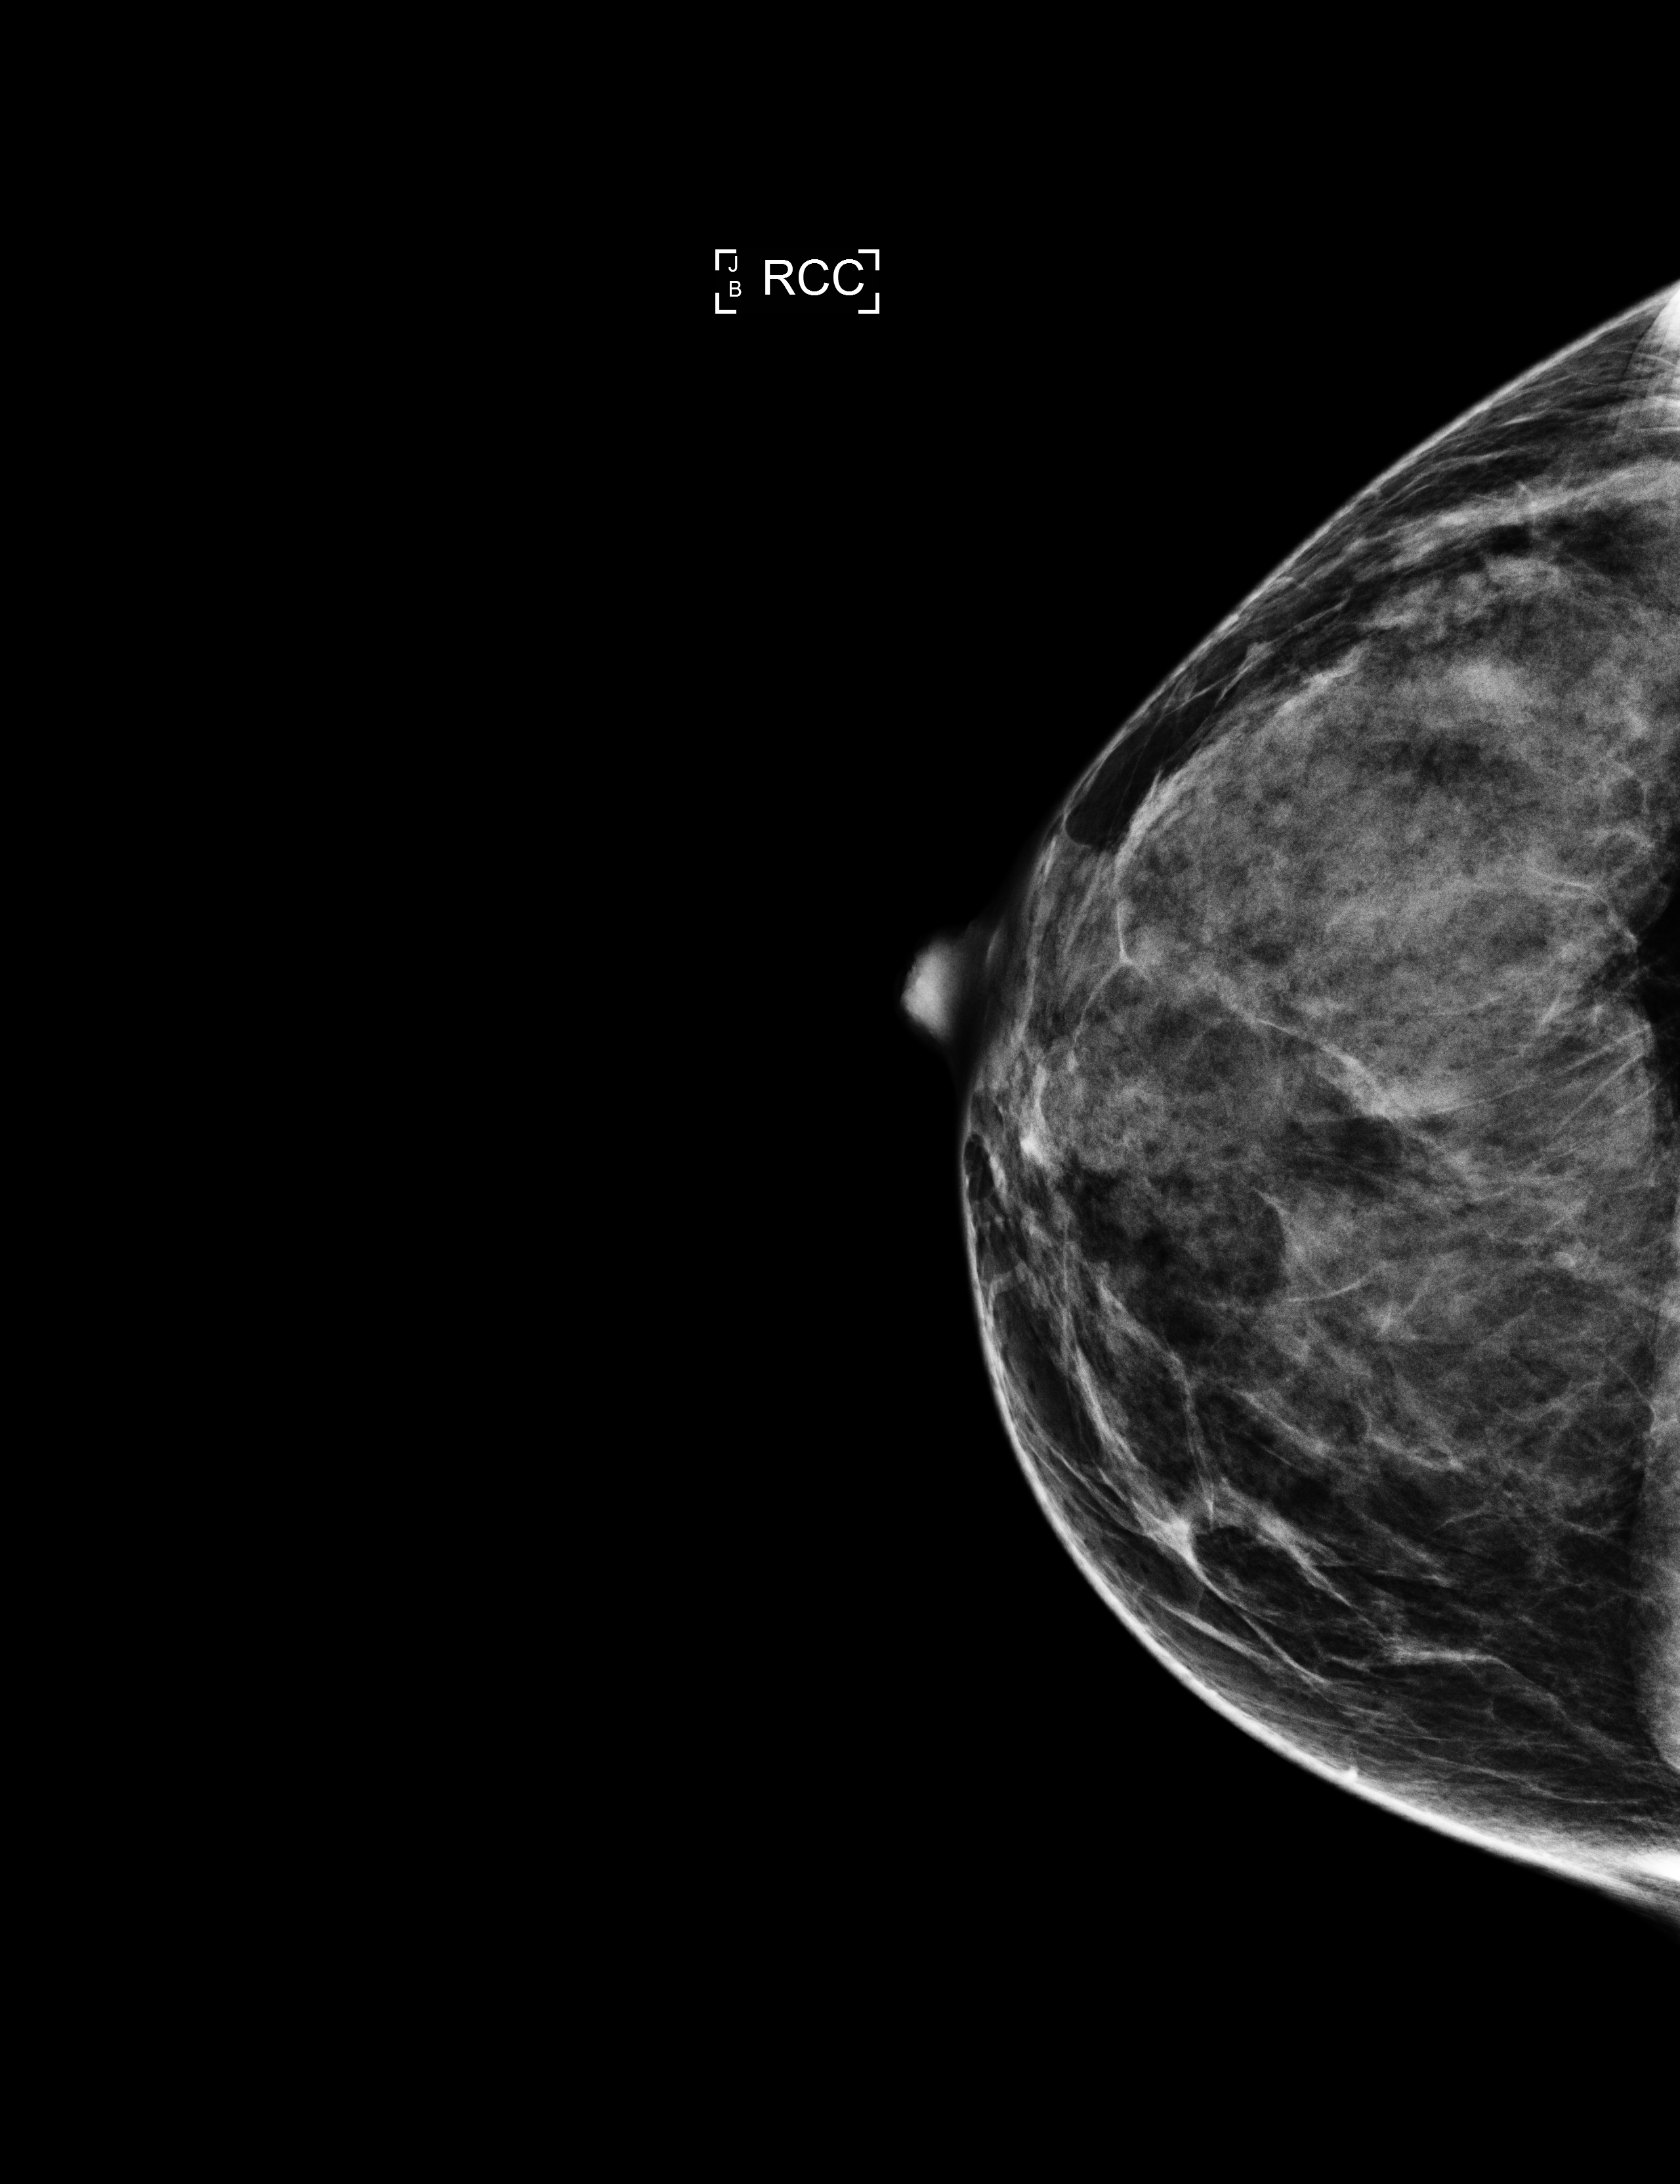
Digital mammogram (FFDM), right breast, cranio-caudal projection, annual screening mammography examination. Patient: female, 46 years.
- BI-RADS breast density category at the screening exam (both breasts, scale 1–4): 4
- final BI-RADS category for the screening round (tomosynthesis exam, both breasts): category 1
- recall: no recall after this screen